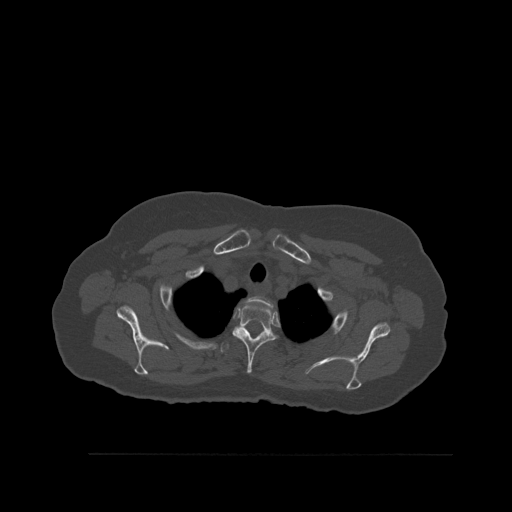
CT including the spine, one axial slice; slice 431 of 527 in the series (ordered by position); bone window (W 1800 / L 400 HU); 1.5 mm slice thickness; 512 × 512 image matrix. Female patient, age 73 years. Case-level facts recorded for this patient, not image findings: primary cancer: breast.
Annotated regions visible in this slice (semi-automatically segmented with operator editing):
- T1 vertebra: bounding box <248,296,273,307> (left, top, right, bottom; pixels)
- T2 vertebra: <228,303,276,374>
- T3 vertebra: <220,341,230,353>